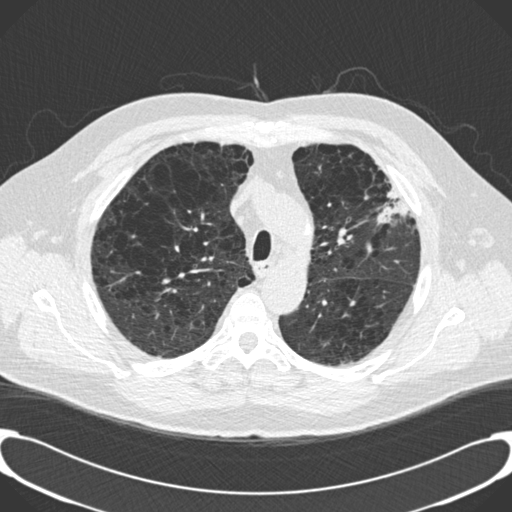
Chest CT (low-dose screening protocol), one axial image; third annual screen; lung window (W 1500 / L -600 HU); 2 mm slice thickness; 120 kVp; slice 43 of 189 in the series; 512 × 512 image matrix. Male, age 59 years at enrolment.
Expert-annotated lung lesion, box from (x=360, y=161) to (x=415, y=225) px. Screening reader's record for this exam: no non-calcified nodule ≥4 mm recorded. Official screen result: positive, other. Lung cancer was diagnosed 134 days after this screen: bronchiolo-alveolar carcinoma, mixed mucinous and non-mucinous, left upper lobe, stage IA (AJCC 6th edition), 20 mm at pathology.